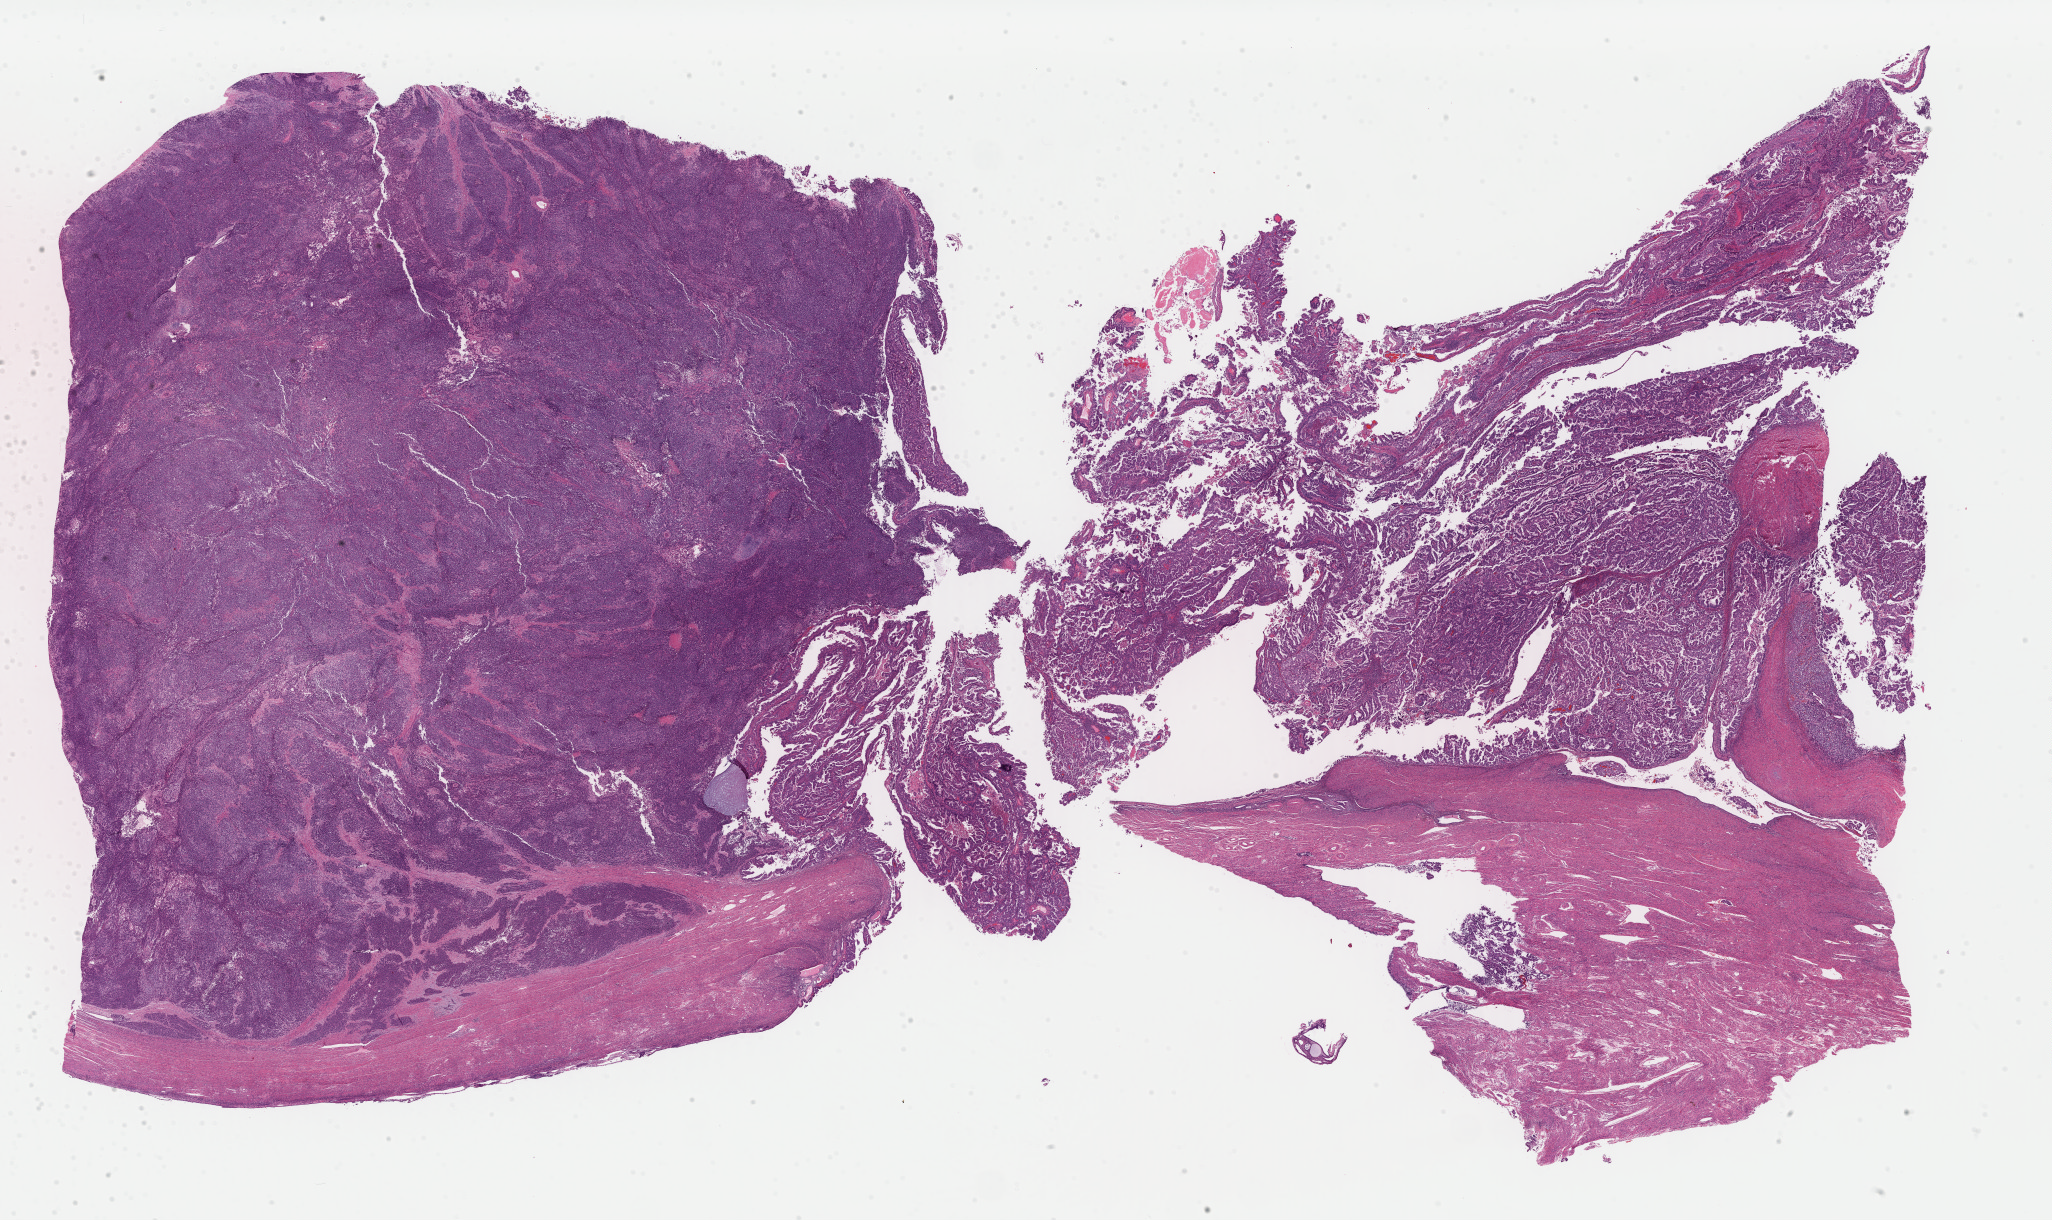
Digitized H&E-stained tissue section (whole slide) — shown as a low-resolution overview of the whole scanned area (about 32.4 x 19.3 mm, acquisition: 40x scan), formalin-fixed paraffin-embedded (FFPE) diagnostic section, primary tumour sample from the uterus. Patient sex: female.
FIGO stage: IC. Histologic diagnosis: Mullerian mixed tumor (endometrium).